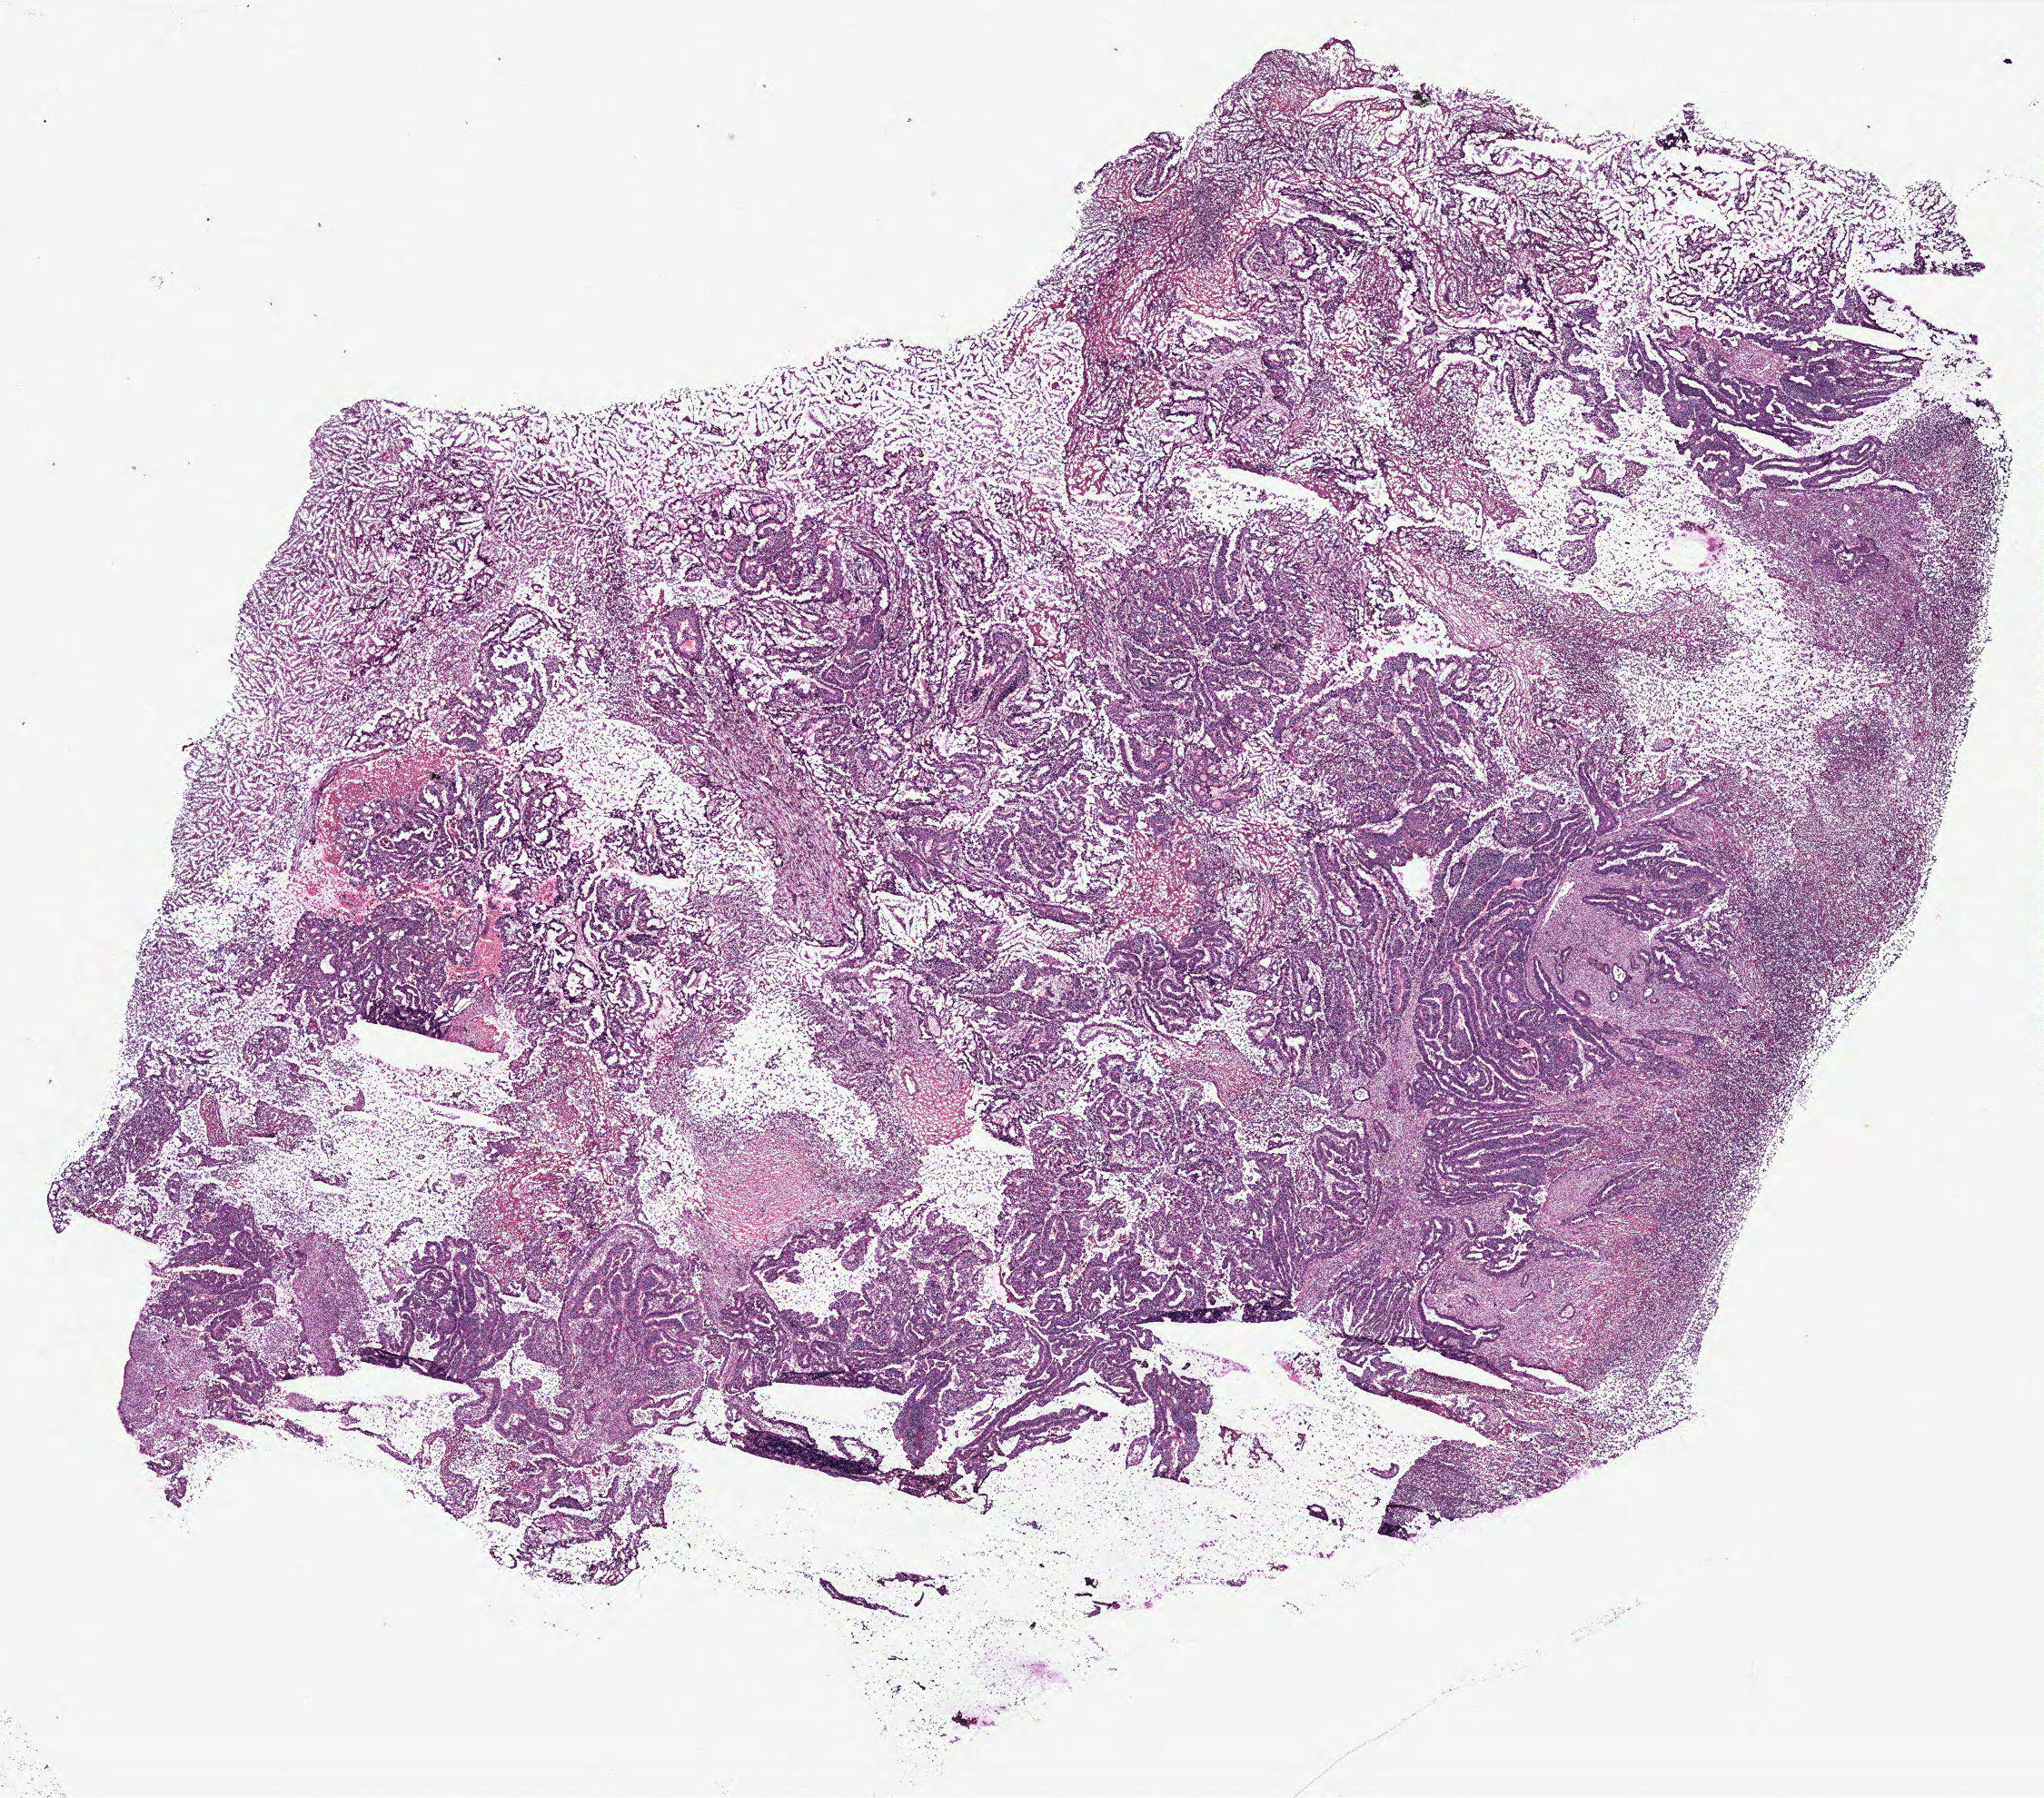
Digitized Hematoxylin and eosin (H&E) stained tissue section (whole slide), shown as a low-resolution overview of the whole scanned area (about 18.0 x 15.8 mm, acquisition: 40x scan), colon, normal (non-tumour) tissue. Female, 65 y/o.
This section: normal (non-tumour) tissue from the same patient. Patient diagnosis: Adenocarcinoma, NOS.